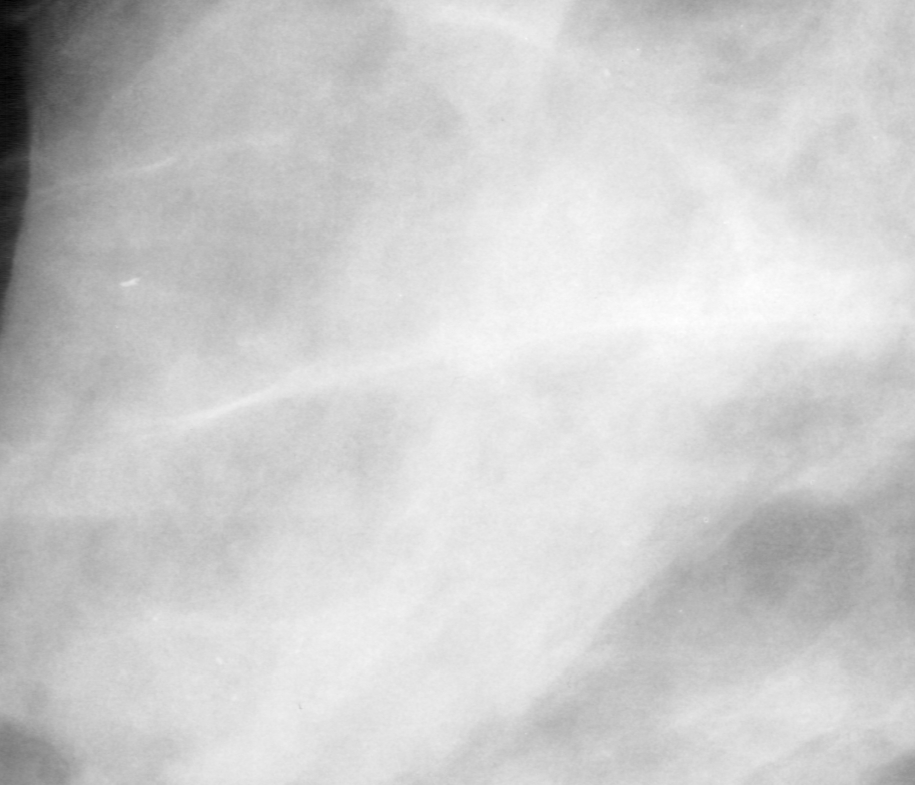
Region of interest cut from a scanned film mammogram (one marked finding), left breast, MLO view.
- Calcifications, morphology punctate, distribution regional; BI-RADS assessment category 4; pathology result (as recorded, not read from the image): malignant.